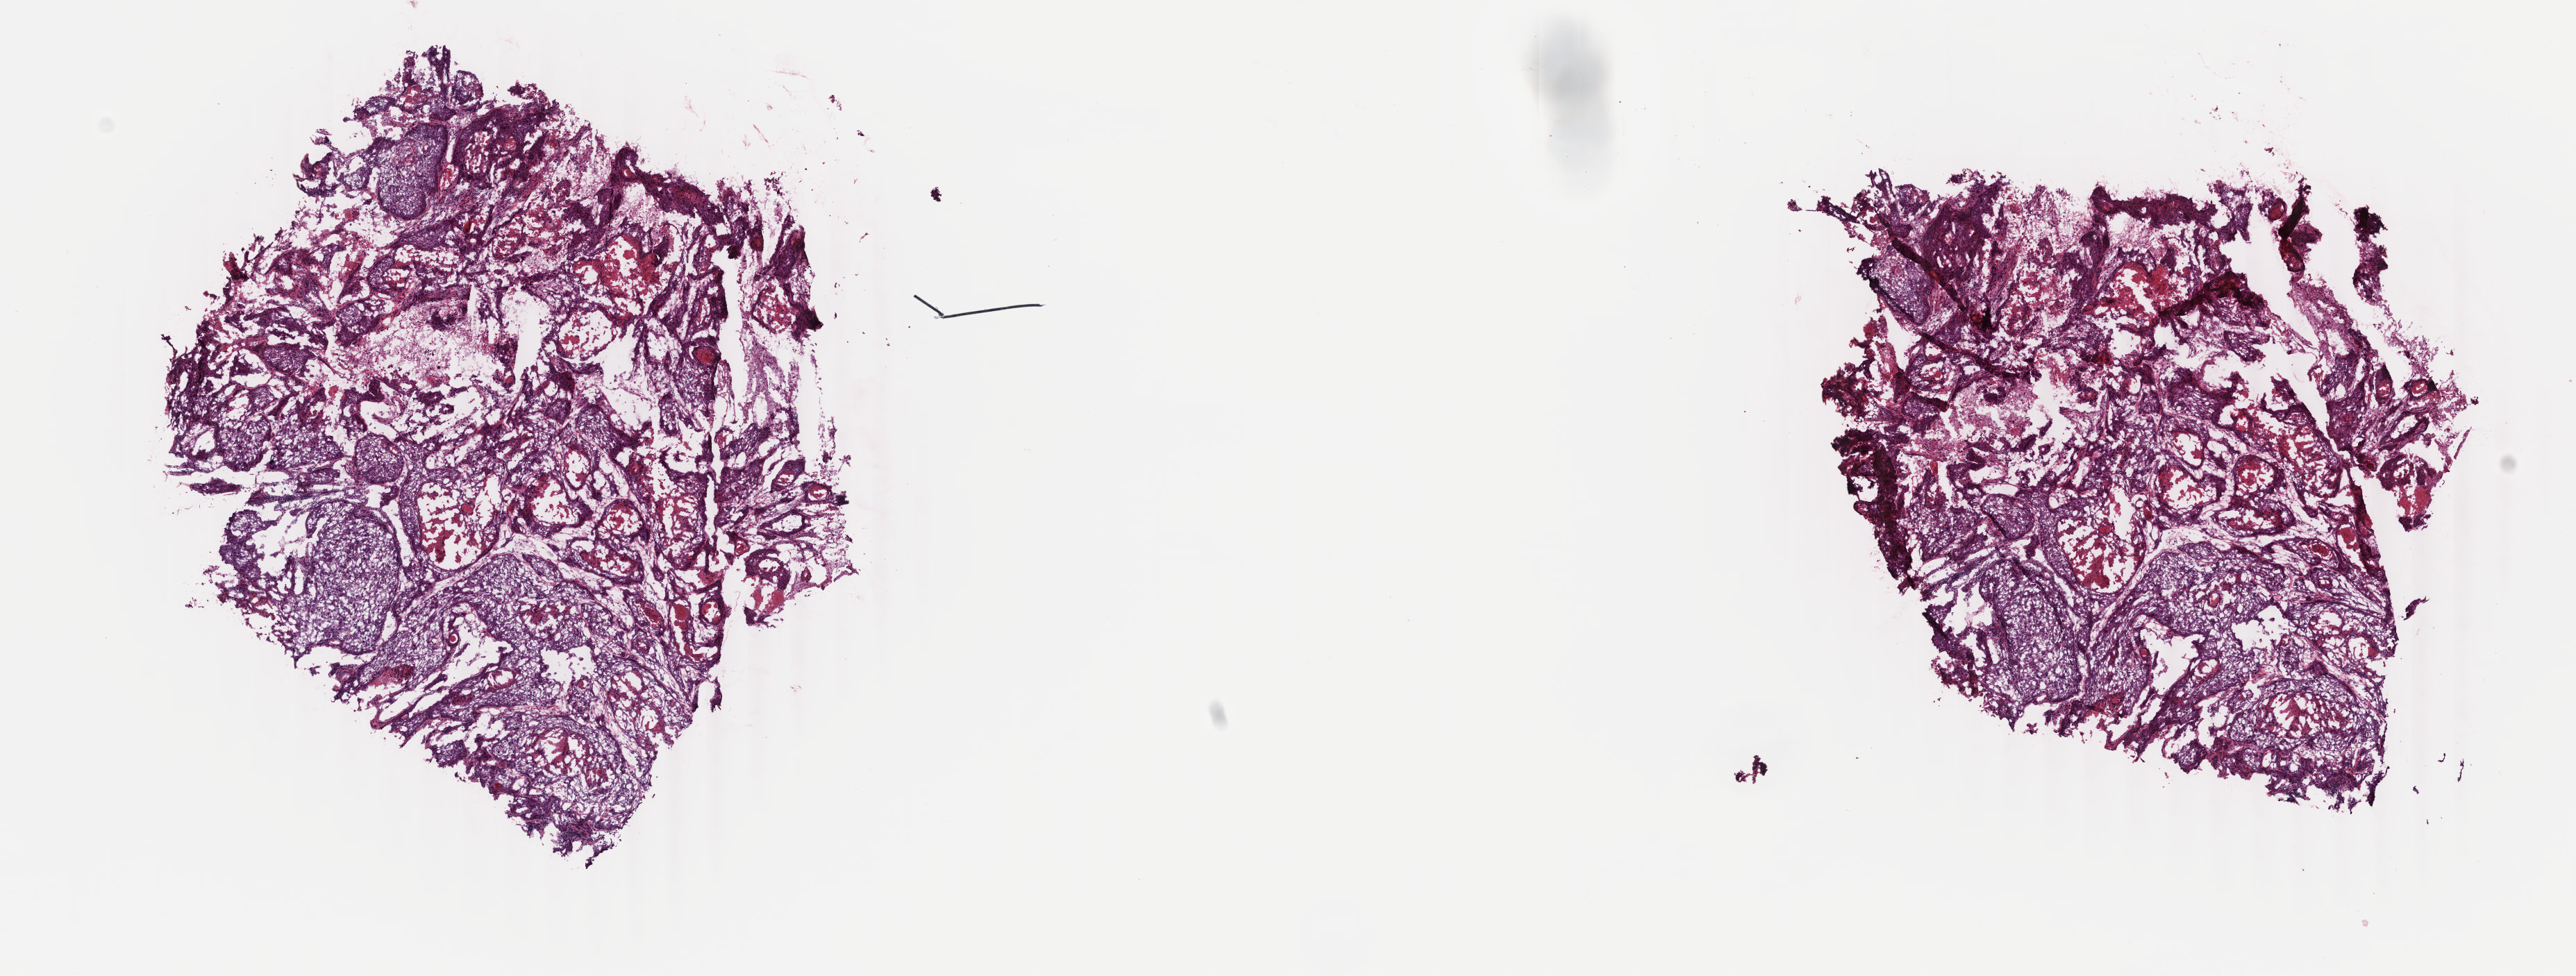
Digitized Hematoxylin and eosin (H&E) stained tissue section (whole slide) — a low-resolution overview of the entire scanned area, about 14.8 x 5.6 mm, frozen section, cervix, primary tumour sample. Female, age 24 years at initial diagnosis. Histologic grade: G3 (poorly differentiated). Slide review estimates, as recorded: tumour cells 85%, tumour nuclei 94%, normal cells 0%, stromal cells 10%, necrosis 5%. Infiltration values recorded for this section: lymphocyte infiltration 2%, monocyte infiltration 0%, neutrophil infiltration 0%.
Histologic diagnosis: Squamous cell carcinoma, keratinizing, NOS (cervix uteri). FIGO stage: IIB.